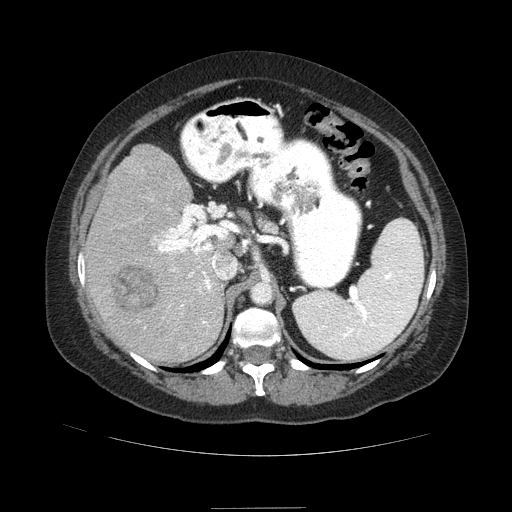
Contrast-enhanced abdominal CT (liver protocol), one axial slice; slice 53 of 89 in the series (ordered by position); reconstruction kernel STANDARD; soft-tissue window (W 400 / L 40 HU); 2.5 mm slice thickness; 512 × 512 image matrix. Case-level facts recorded for this patient, not image findings: diagnosis: hepatocellular carcinoma (patient treated with transarterial chemoembolisation; whether this scan precedes or follows treatment is not stated here); TNM stage (as recorded): Stage-IIIB.
Structures marked on this image (semi-automatic segmentation, software-assisted and operator-edited):
- liver parenchyma outside the tumour (the mass and vessels are separate outlines, so this box may not span the whole liver): bounding box <84,144,231,362> (left, top, right, bottom; pixels)
- mass: <113,266,158,314>
- liver vessels: <152,228,219,325>